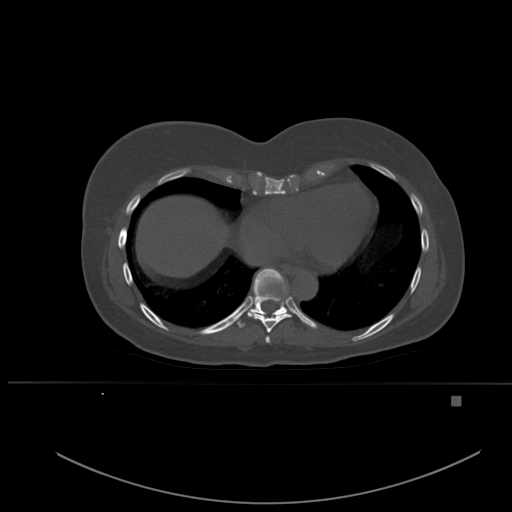
CT including the spine, one axial slice; slice 314 of 651 in the series (ordered by position); bone window (W 1800 / L 400 HU); 1.5 mm slice thickness; 512 × 512 image matrix. Female patient, age 49 years. From the clinical record (not read from this slice): primary cancer: breast; vertebrae with lytic lesions (as recorded): L3, T12, L4.
Structures marked on this image (semi-automatic segmentation, software-assisted and operator-edited):
- T7 vertebra: bounding box <265,336,270,343> (left, top, right, bottom; pixels)
- T8 vertebra: <249,285,292,333>
- T9 vertebra: <226,268,287,328>